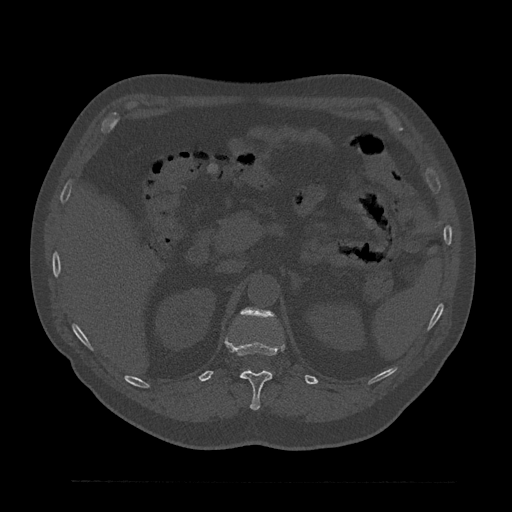
CT including the spine, one axial slice. Reconstruction kernel Br40s/3. 120 kVp. Bone window (W 1800 / L 400 HU). 0.5 mm slice thickness. 512 × 512 image matrix, field of view 430 × 430 mm. Patient: male, 61 years. Case-level facts recorded for this patient, not image findings: primary cancer: prostate.
Annotated regions visible in this slice (semi-automatic segmentation, software-assisted and operator-edited):
- L1 vertebra: bounding box [x1, y1, x2, y2] px = [242, 307, 275, 316]
- T12 vertebra: [225, 338, 285, 410]